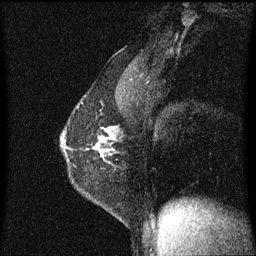
Breast MRI (dynamic contrast-enhanced), one sagittal slice. Position 40 of 60 along the scan axis. Dynamic contrast-enhanced series, image 2 of 3 at this slice position (ordered by acquisition). 1.5 T. TE 4.2 ms, TR 8.4 ms. 256 × 256 image matrix. Female patient, age 40 years.
Structures marked on this image (semi-automatically segmented with operator editing):
- analysis volume of interest (the breast-tissue region the enhancement analysis was run in; not a lesion): bounding box (x1, y1, x2, y2) in pixels: (61, 110, 116, 189)
- tumour enhancement mask (voxels above the 70 % enhancement threshold inside the analysis volume of interest): (61, 126, 115, 157)